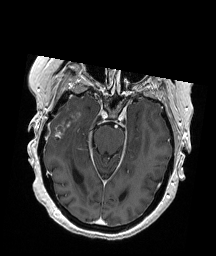
Brain MRI from a brain-tumour surgery series, one axial slice; position 127 of 192 along the scan axis; T1-weighted post-contrast; 1 mm slice thickness; 216 × 256 image matrix, field of view 211 × 250 mm. From the clinical record (not read from this slice): histopathology: Glioblastoma; WHO grade: 4; IDH mutation: no; tumour location: Right Temporal.
Annotated regions visible in this slice (expert manual segmentation):
- tumour: bounding box (x1, y1, x2, y2) in pixels: (54, 114, 80, 139)